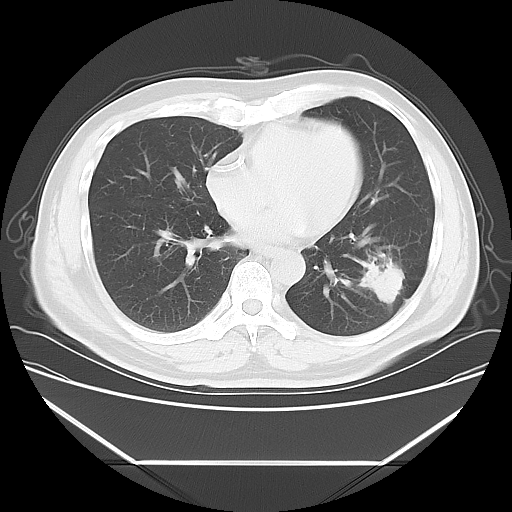
Chest CT, one axial slice. Position 24 of 57 along the scan axis. 120 kVp. Lung window (W 1500 / L -600 HU). 5 mm slice thickness. 512 × 512 image matrix, field of view 384 × 384 mm. Patient: male, 53 years. Case-level facts recorded for this patient, not image findings: clinical TNM (as recorded): T1c N0 M0; histopathological grade: G2-3.
Annotated regions visible in this slice (bounding box drawn by a radiologist):
- lung tumour (recorded histology: adenocarcinoma): bounding box <353,250,410,312> (left, top, right, bottom; pixels)